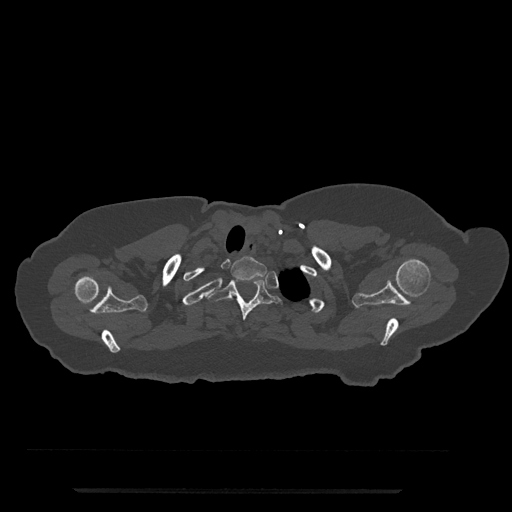
CT including the spine, one axial slice; slice 684 of 797 in the series (ordered by position); reconstruction kernel Br40s/3; bone window (W 1800 / L 400 HU); 512 × 512 image matrix, field of view 440 × 440 mm. Female patient, age 51 years. Case-level facts recorded for this patient, not image findings: primary cancer: neuro.
Outlined on this slice (semi-automatic segmentation, software-assisted and operator-edited):
- T1 vertebra: bounding box (x1, y1, x2, y2) in pixels: (231, 256, 267, 281)
- T2 vertebra: (206, 274, 283, 321)